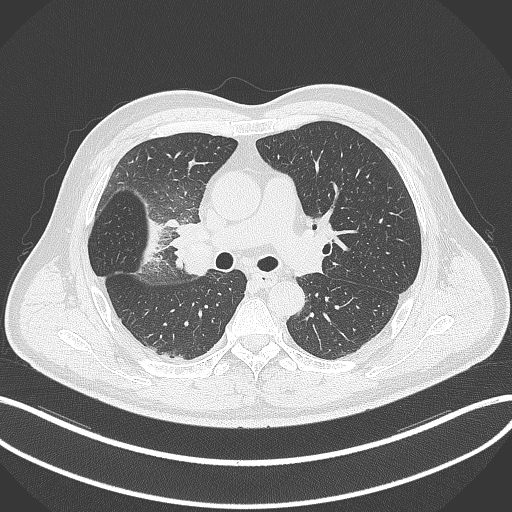
Chest CT, one axial slice; slice 197 of 348 in the series (ordered by position); lung window (W 1500 / L -600 HU); 1 mm slice thickness; 512 × 512 image matrix, field of view 400 × 400 mm. Patient: male, 55 years. From the clinical record (not read from this slice): clinical TNM (as recorded): T3 N2 M1.
Annotated regions visible in this slice (rectangle marked by the reading radiologist):
- lung tumour (recorded histology: adenocarcinoma): bounding box [x1, y1, x2, y2] px = [139, 214, 162, 275]